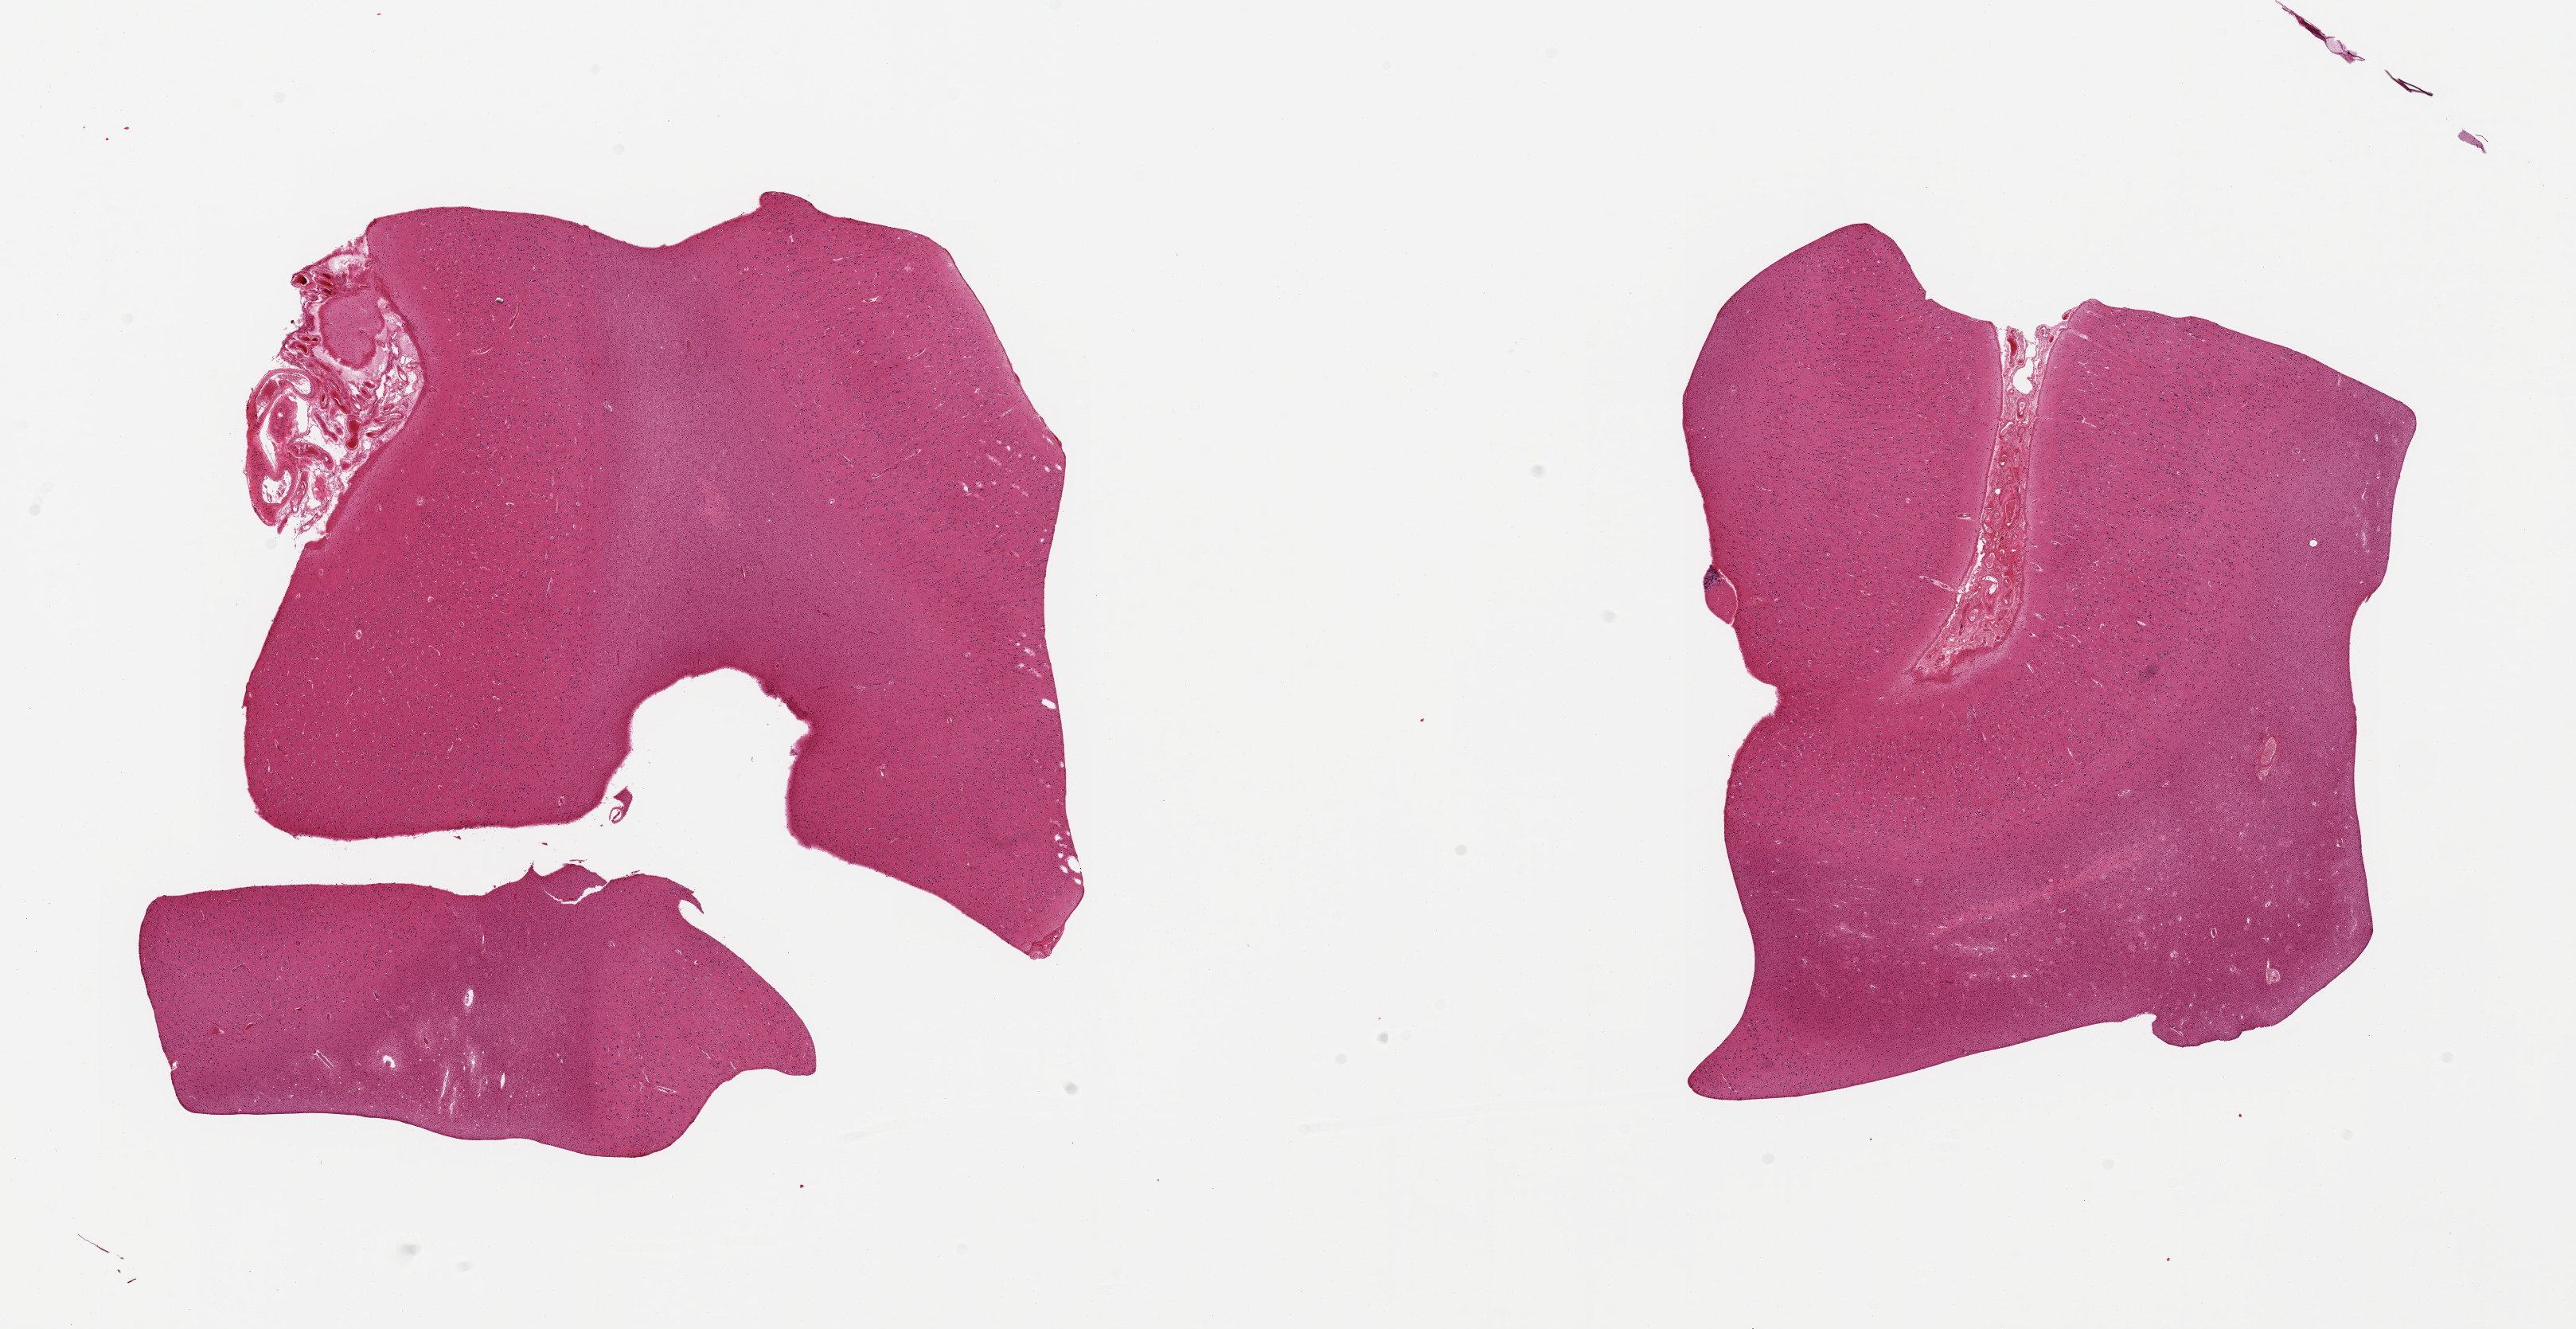
Whole-slide image, haematoxylin and eosin stain, low-resolution overview of the scanned area, about 25.6 x 13.2 mm, PAXgene-fixed, paraffin-embedded tissue, section of cerebral cortex (target tissue), tissue donor sample.
- review note (as recorded): 3 pieces (fragmented); cortex with small portion of meninges, not pituitary